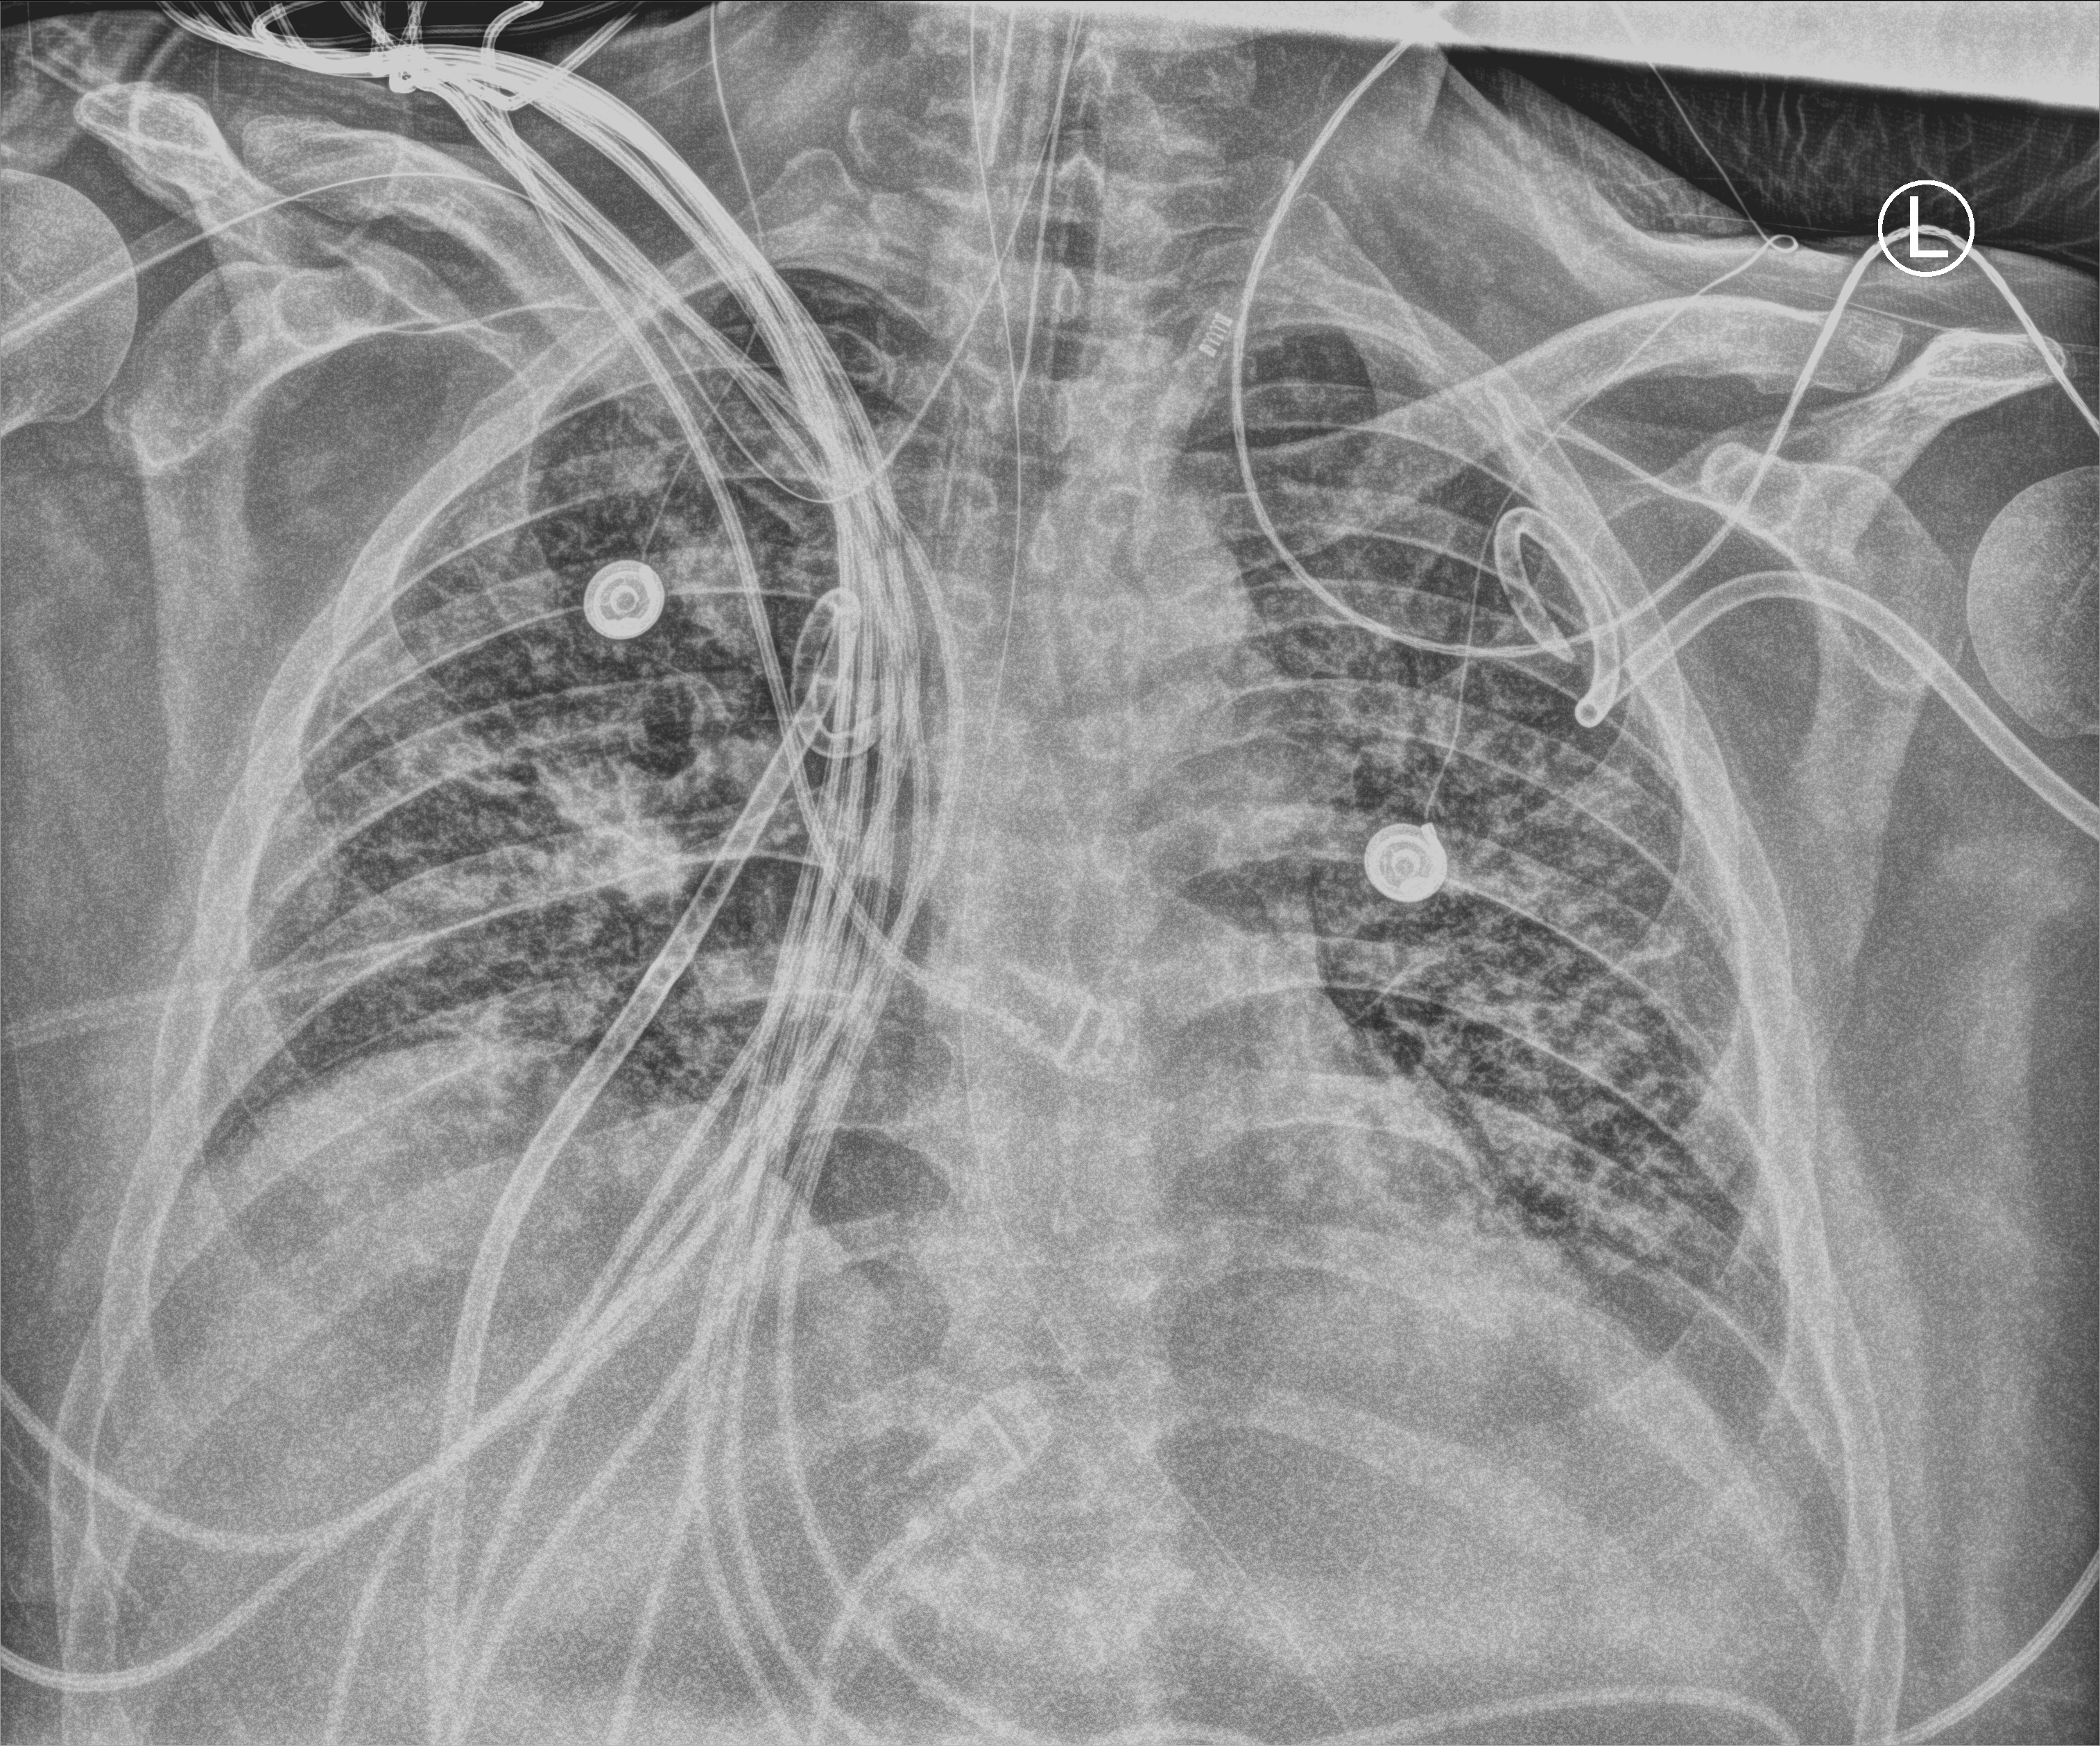
Chest X-ray (portable). Adult patient hospitalised with COVID-19, age 18–59 years.
From the hospital-stay record, not from the radiograph (when in the stay this image was taken is not recorded): mechanically ventilated during this hospital stay: yes.